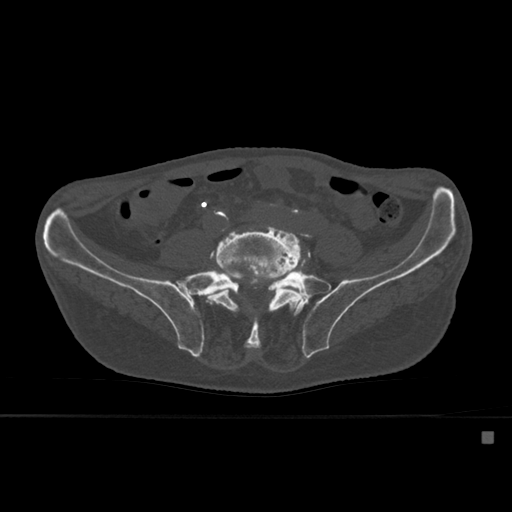
CT including the spine, one axial slice; slice 170 of 527 in the series (ordered by position); bone window (W 1800 / L 400 HU); 1.5 mm slice thickness; 512 × 512 image matrix. Male patient, age 78 years. Case-level facts recorded for this patient, not image findings: primary cancer: prostate.
Structures marked on this image (semi-automatically segmented with operator editing):
- L5 vertebra: bounding box [x1, y1, x2, y2] px = [207, 227, 305, 349]